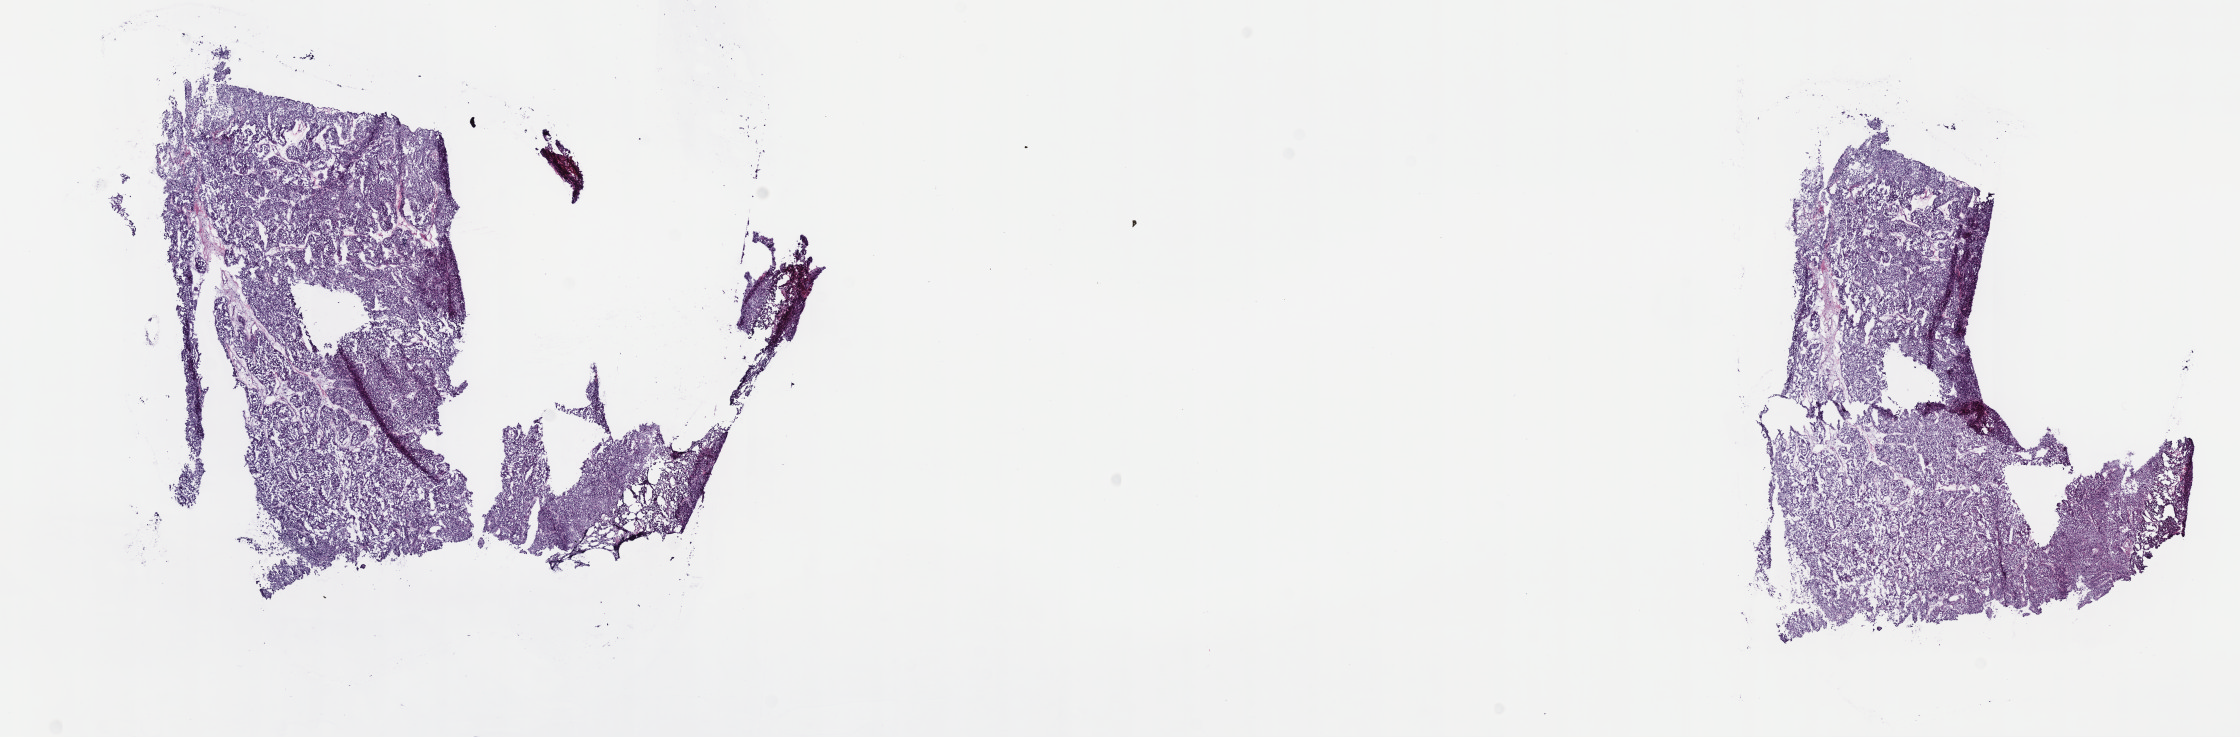
H&E whole-slide image, whole scanned area (about 18.1 x 6.0 mm, from a 40x scan) shown as a low-resolution overview; frozen section from the top of the tissue portion; primary tumour sample from the kidney. Patient: male, age at initial diagnosis 50 years. Slide review estimates, as recorded: tumour cells 95%, tumour nuclei 95%, normal cells 0%, stromal cells 3%, necrosis 2%. Inflammatory infiltration, as recorded: lymphocyte infiltration 2%, monocyte infiltration 2%, neutrophil infiltration 0%.
AJCC pathologic stage: I (6th edition). Histologic diagnosis: Papillary adenocarcinoma, NOS.